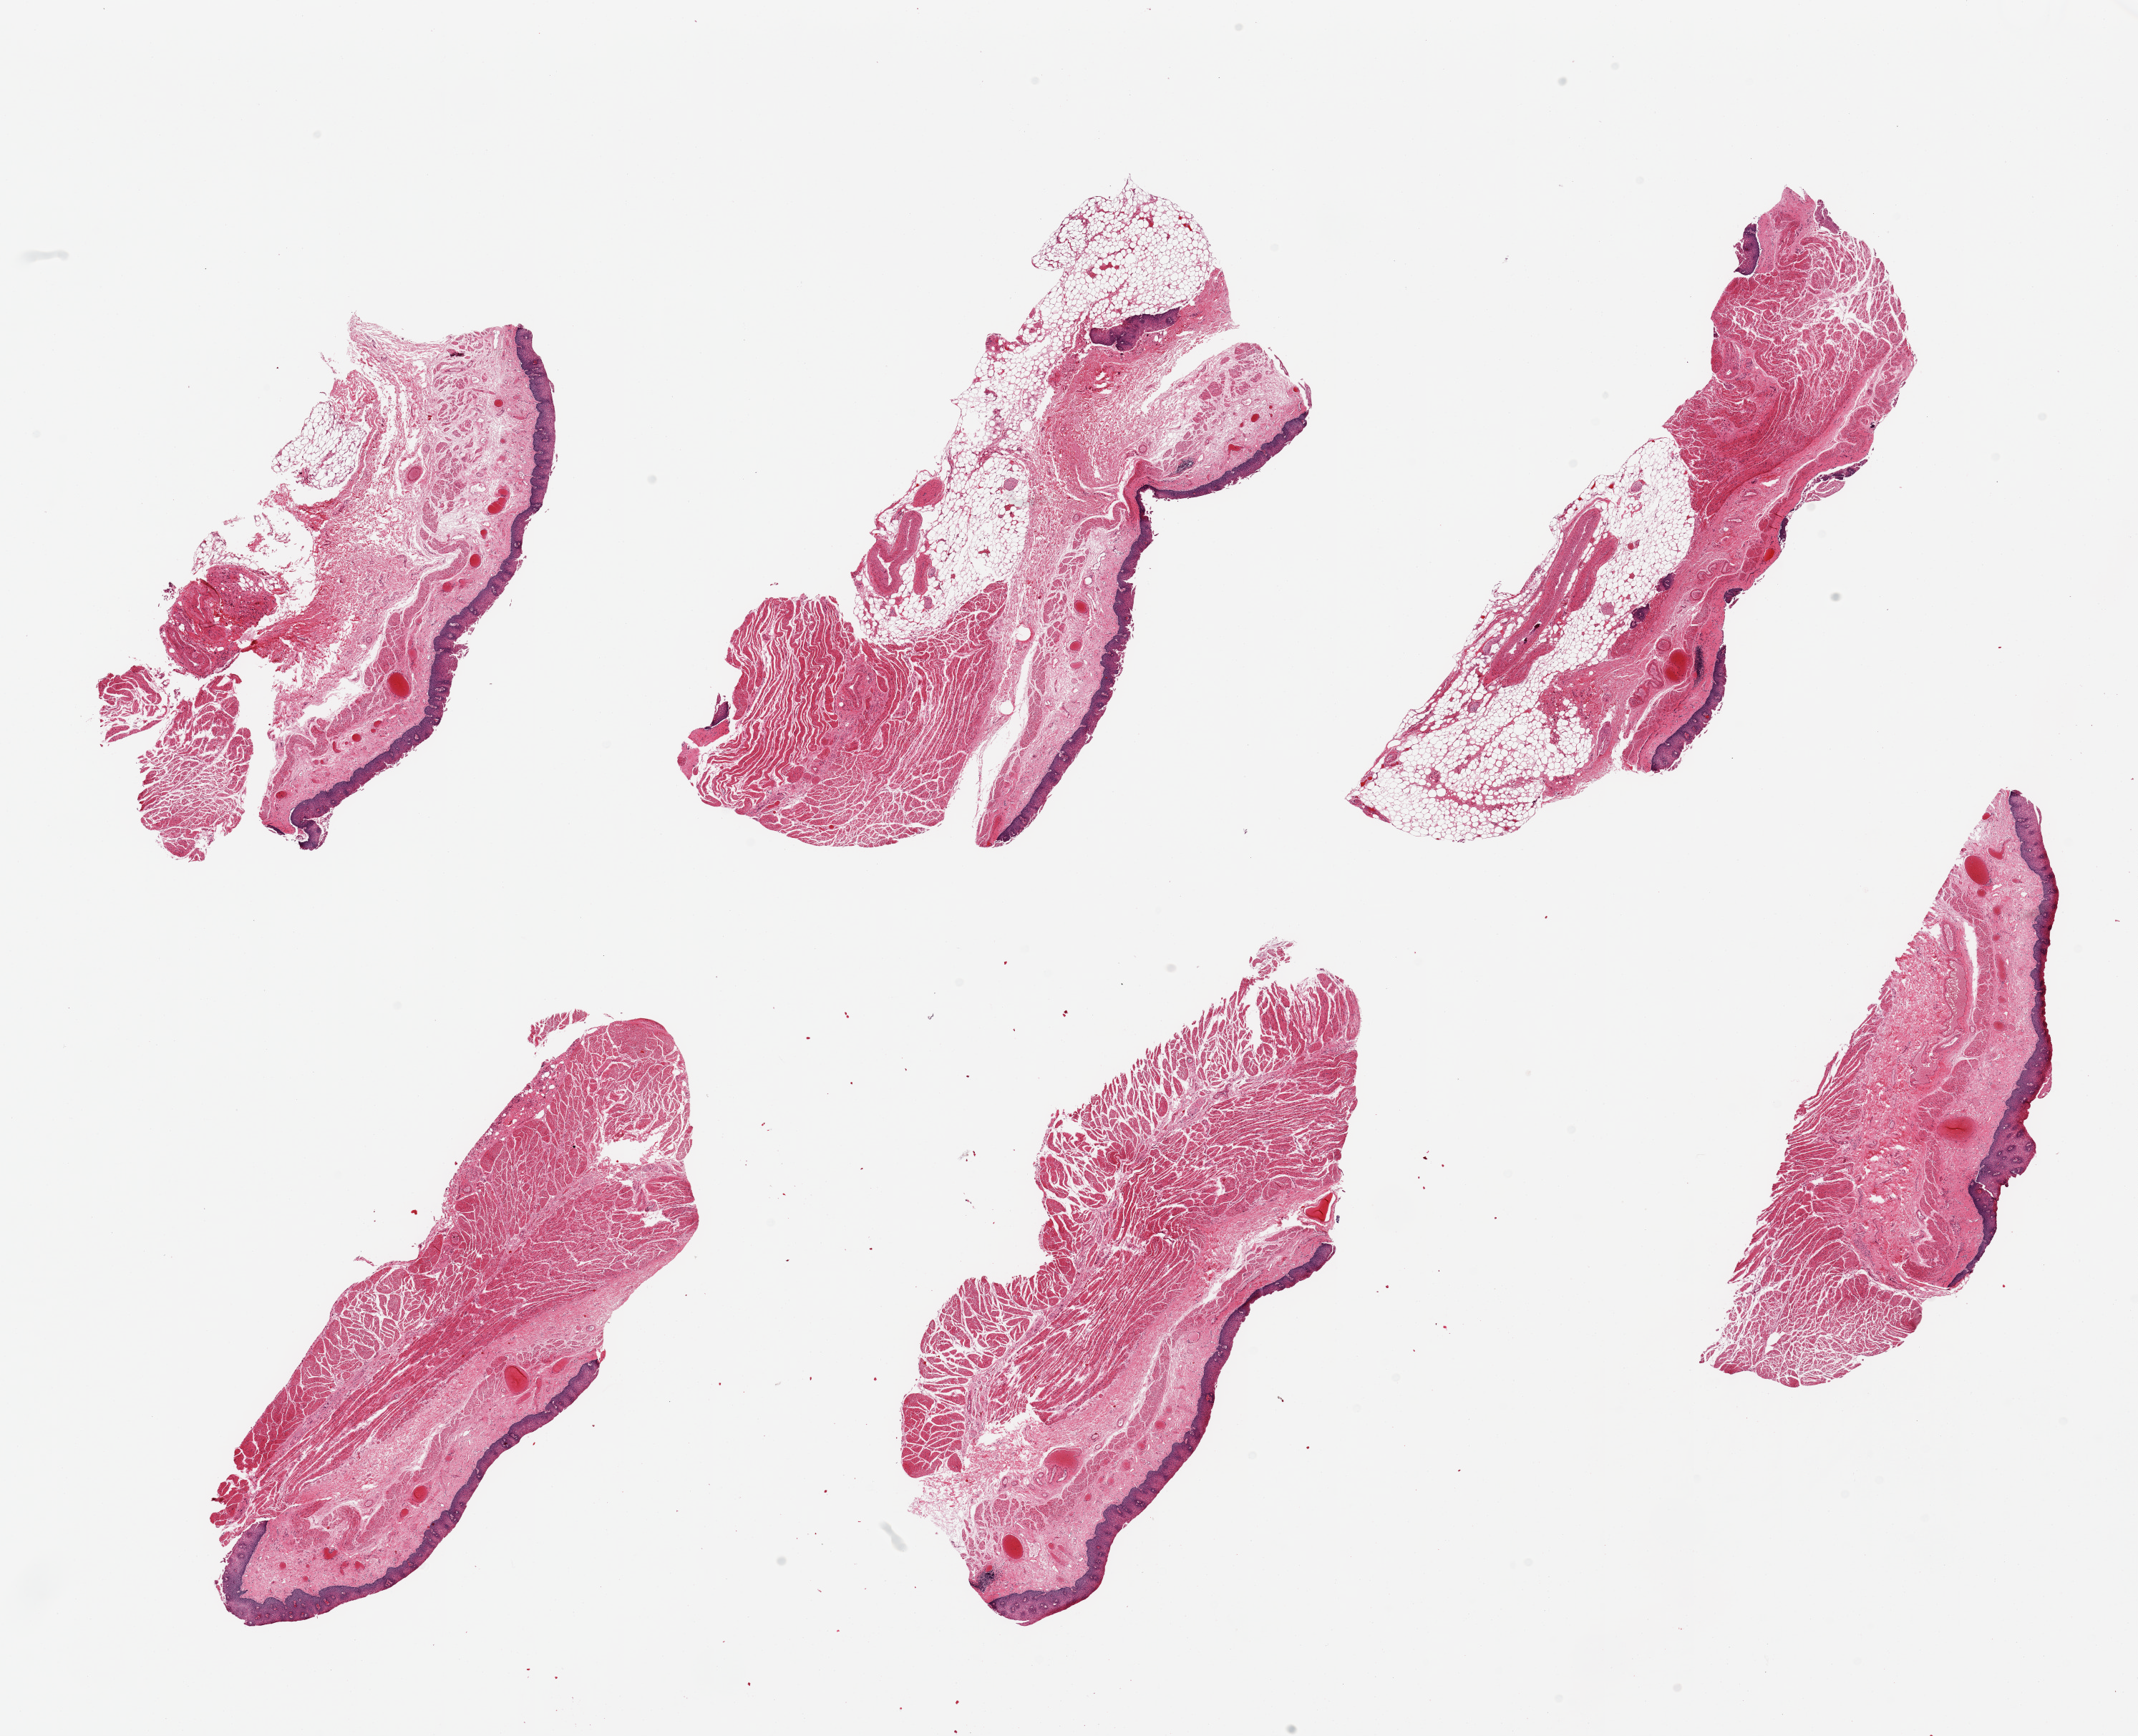
Haematoxylin and eosin whole-slide image, low-resolution overview of the scanned area, about 23.6 x 19.2 mm, PAXgene-fixed, paraffin-embedded tissue, section of gastroesophageal junction (target tissue), tissue donor sample. Male donor.
- review note (as recorded): 6 pieces, only ~50% target muscularis, squamous mucosa present